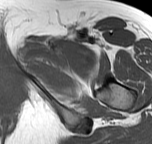
MRI of an extremity soft-tissue mass, one axial slice. Slice 48 of 57 in the series (ordered by position). MR volume resampled by the dataset authors to the PET/CT grid (not the native acquisition matrix). 3.27 mm slice thickness. 152 × 144 image matrix. Female patient. Case-level facts recorded for this patient, not image findings: histological type: pleiomorphic leiomyosarcoma; grade: intermediate; site of the primary tumour: left thigh.
Annotated regions visible in this slice (expert contour drawn on MRI and transferred to this co-registered scan by the dataset authors):
- gross tumour volume including surrounding oedema: bounding box <25,44,48,57> (left, top, right, bottom; pixels)